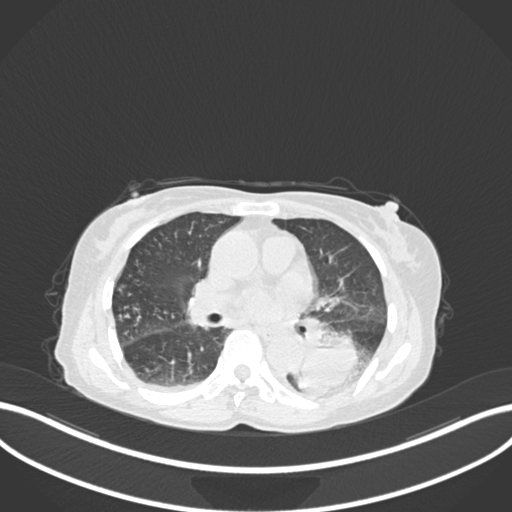
Chest CT, one axial slice. Position 88 of 233 along the scan axis. Lung window (W 1500 / L -600 HU). 1 mm slice thickness. 512 × 512 image matrix. Patient: female, 78 years. Case-level facts recorded for this patient, not image findings: clinical TNM (as recorded): T3 N0 M1.
Structures marked on this image (bounding box drawn by a radiologist):
- lung tumour (recorded histology: squamous cell carcinoma): bounding box (x1, y1, x2, y2) in pixels: (294, 331, 369, 400)